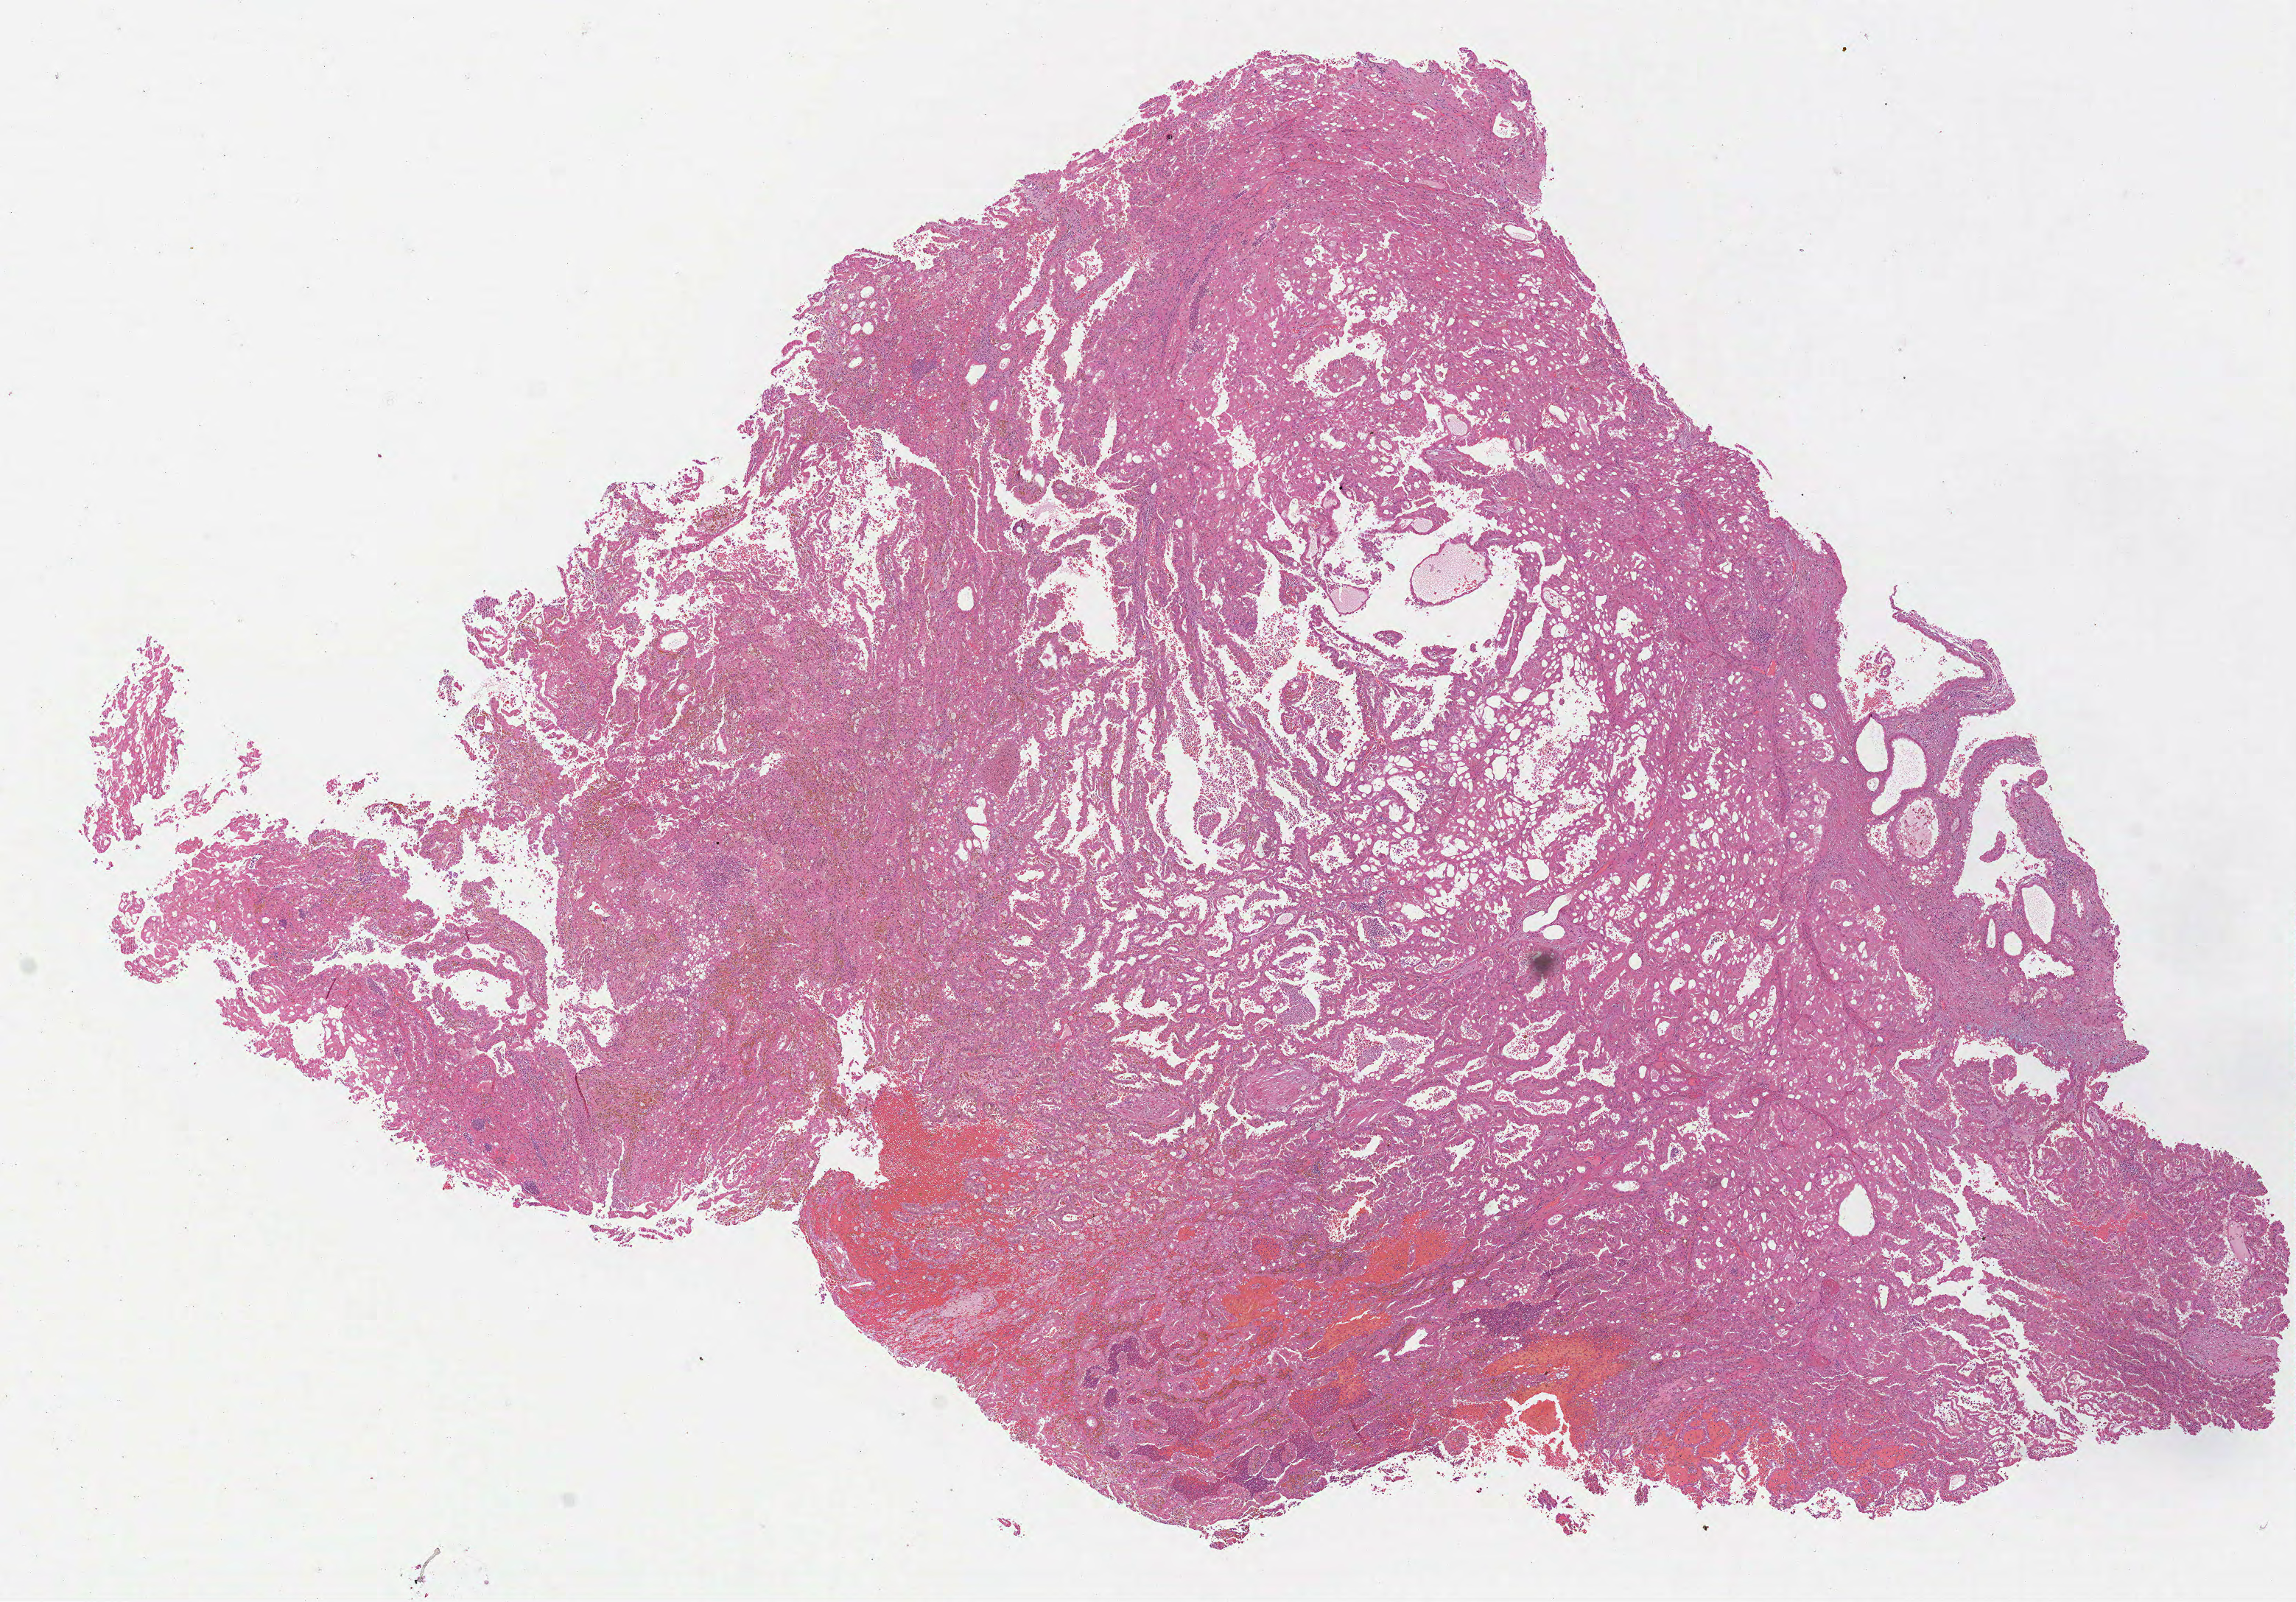
H&E whole-slide image — low-resolution overview of the scanned area, about 12.6 x 8.8 mm (acquisition: 40x scan), formalin-fixed paraffin-embedded (FFPE) diagnostic section, primary tumour sample from the kidney. Patient: male, age at initial diagnosis 48 years.
Pathologic diagnosis: Papillary adenocarcinoma, NOS.